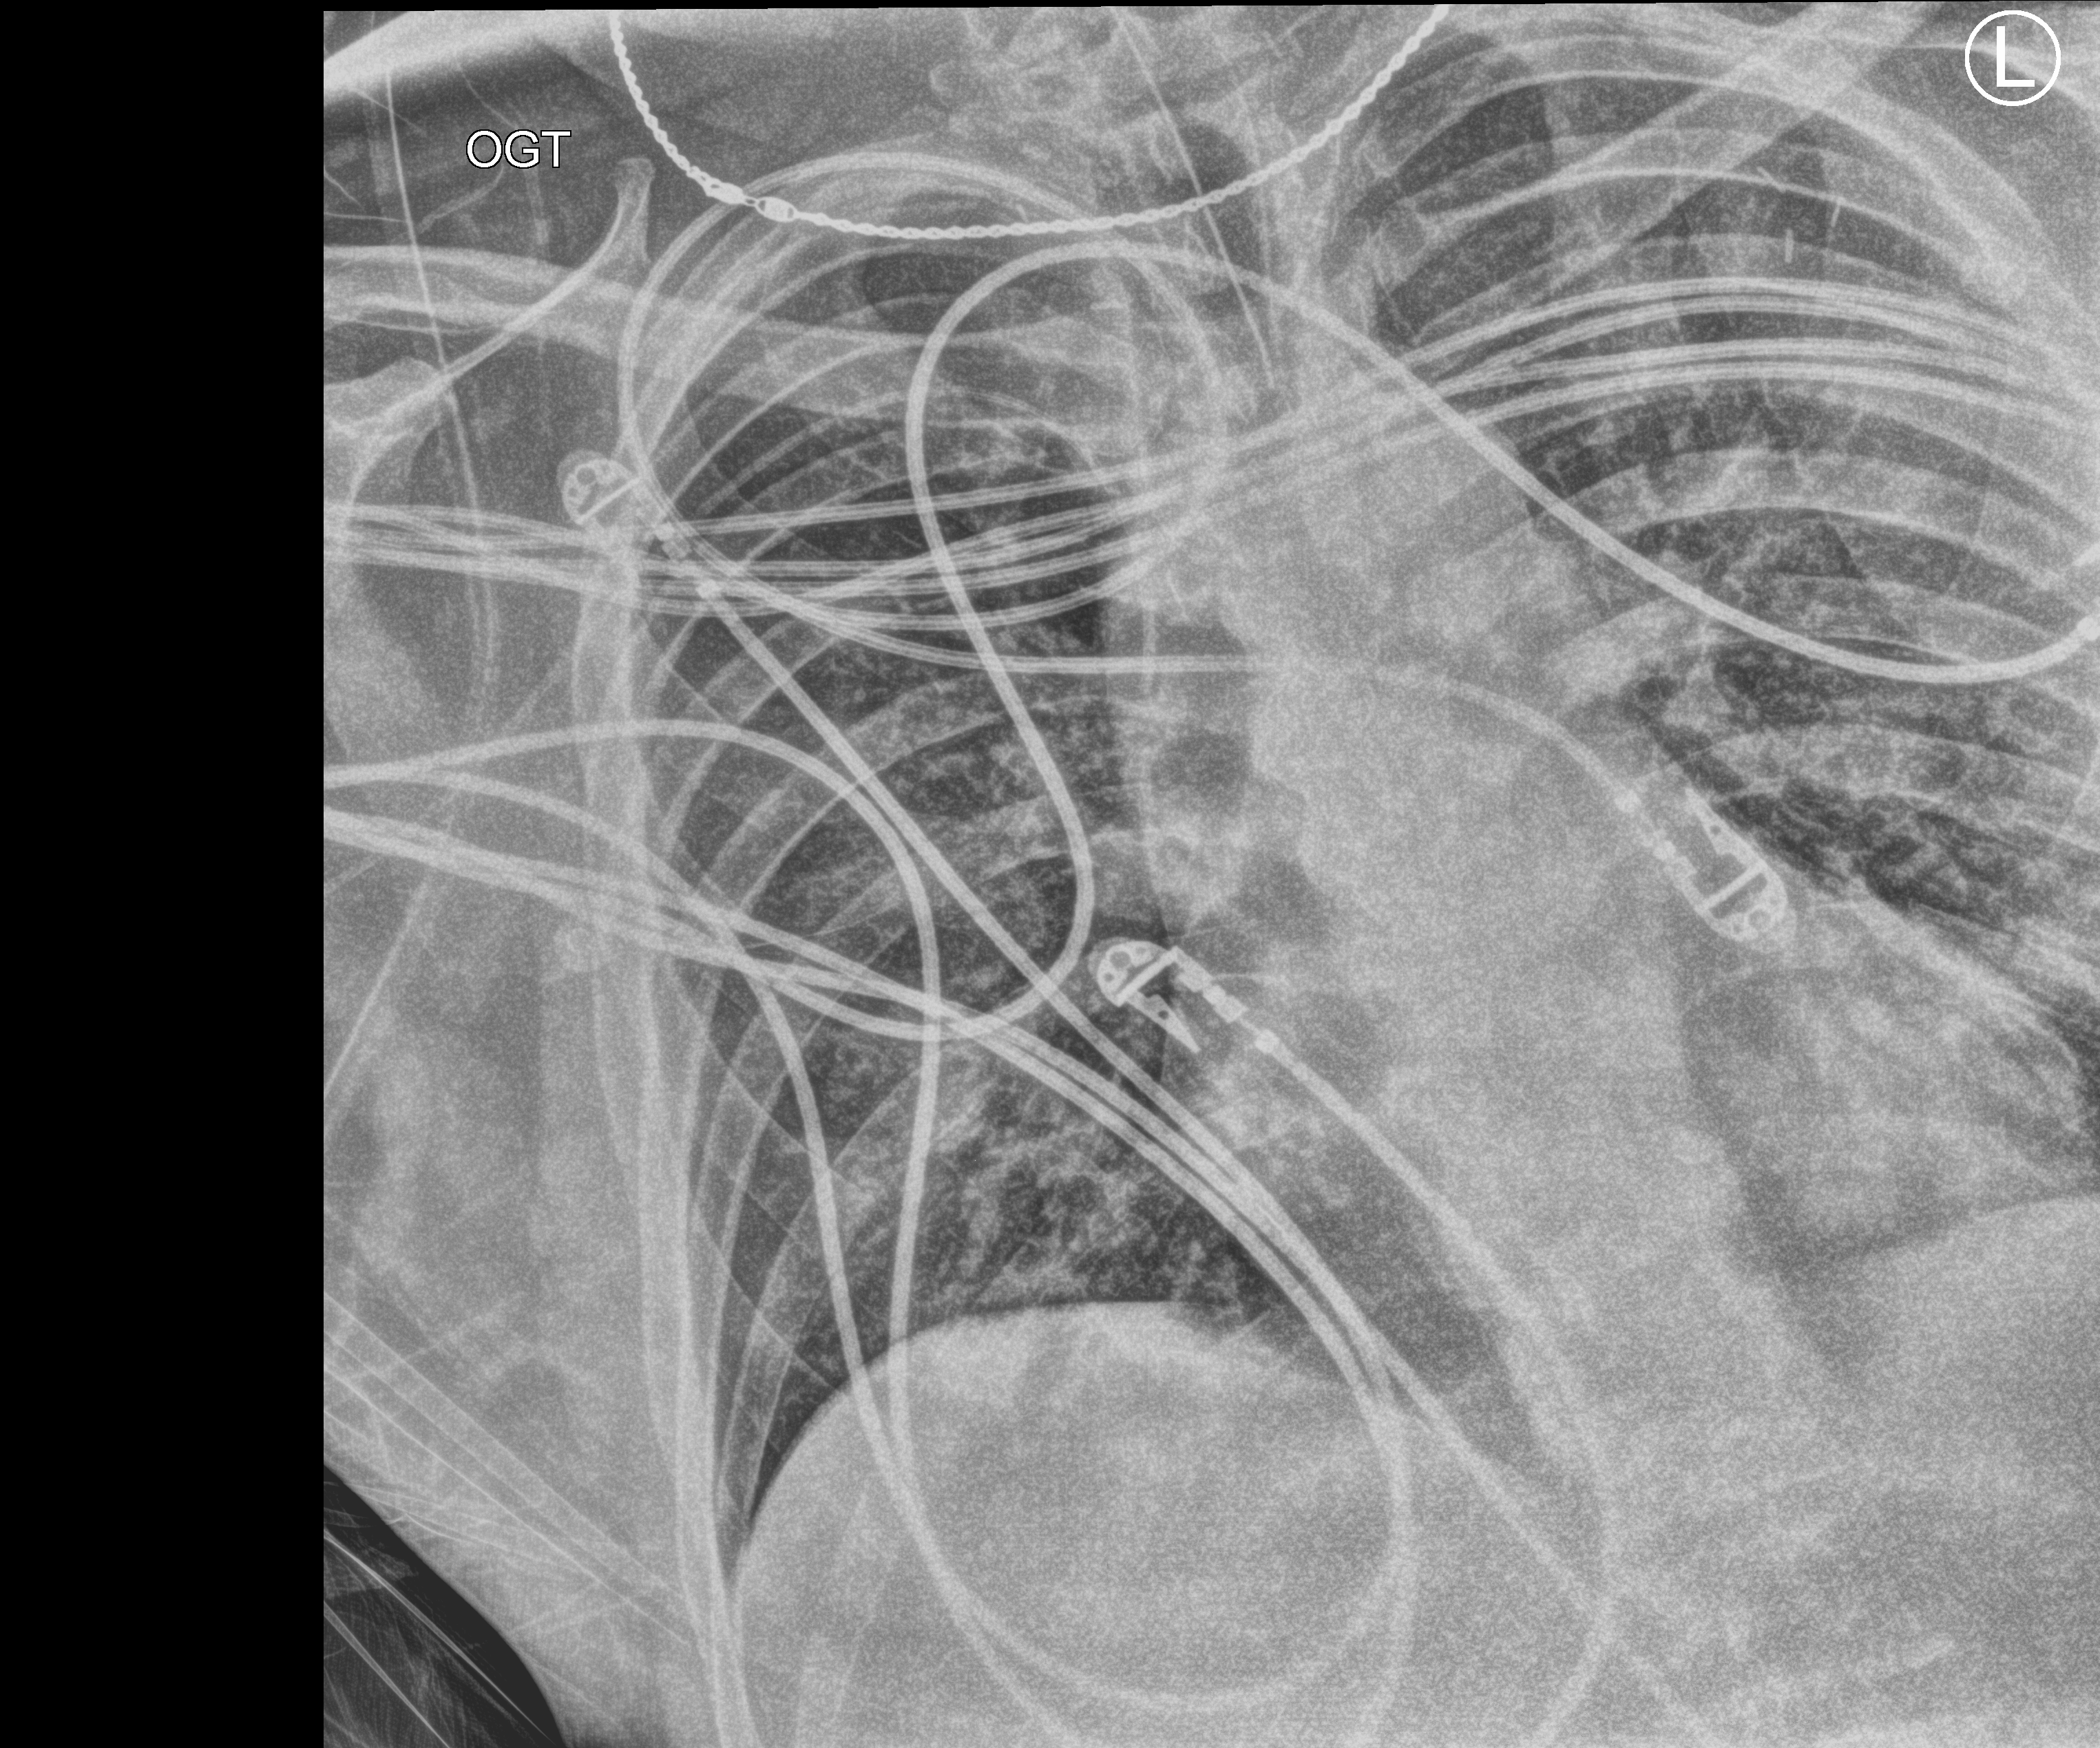
Bedside chest radiograph (computed radiography). Adult patient hospitalised with COVID-19, age 18–59 years.
From the hospital-stay record, not from the radiograph (when in the stay this image was taken is not recorded): other chronic lung disease (admission record): no; admitted to intensive care during this hospital stay: yes; mechanically ventilated during this hospital stay: yes.